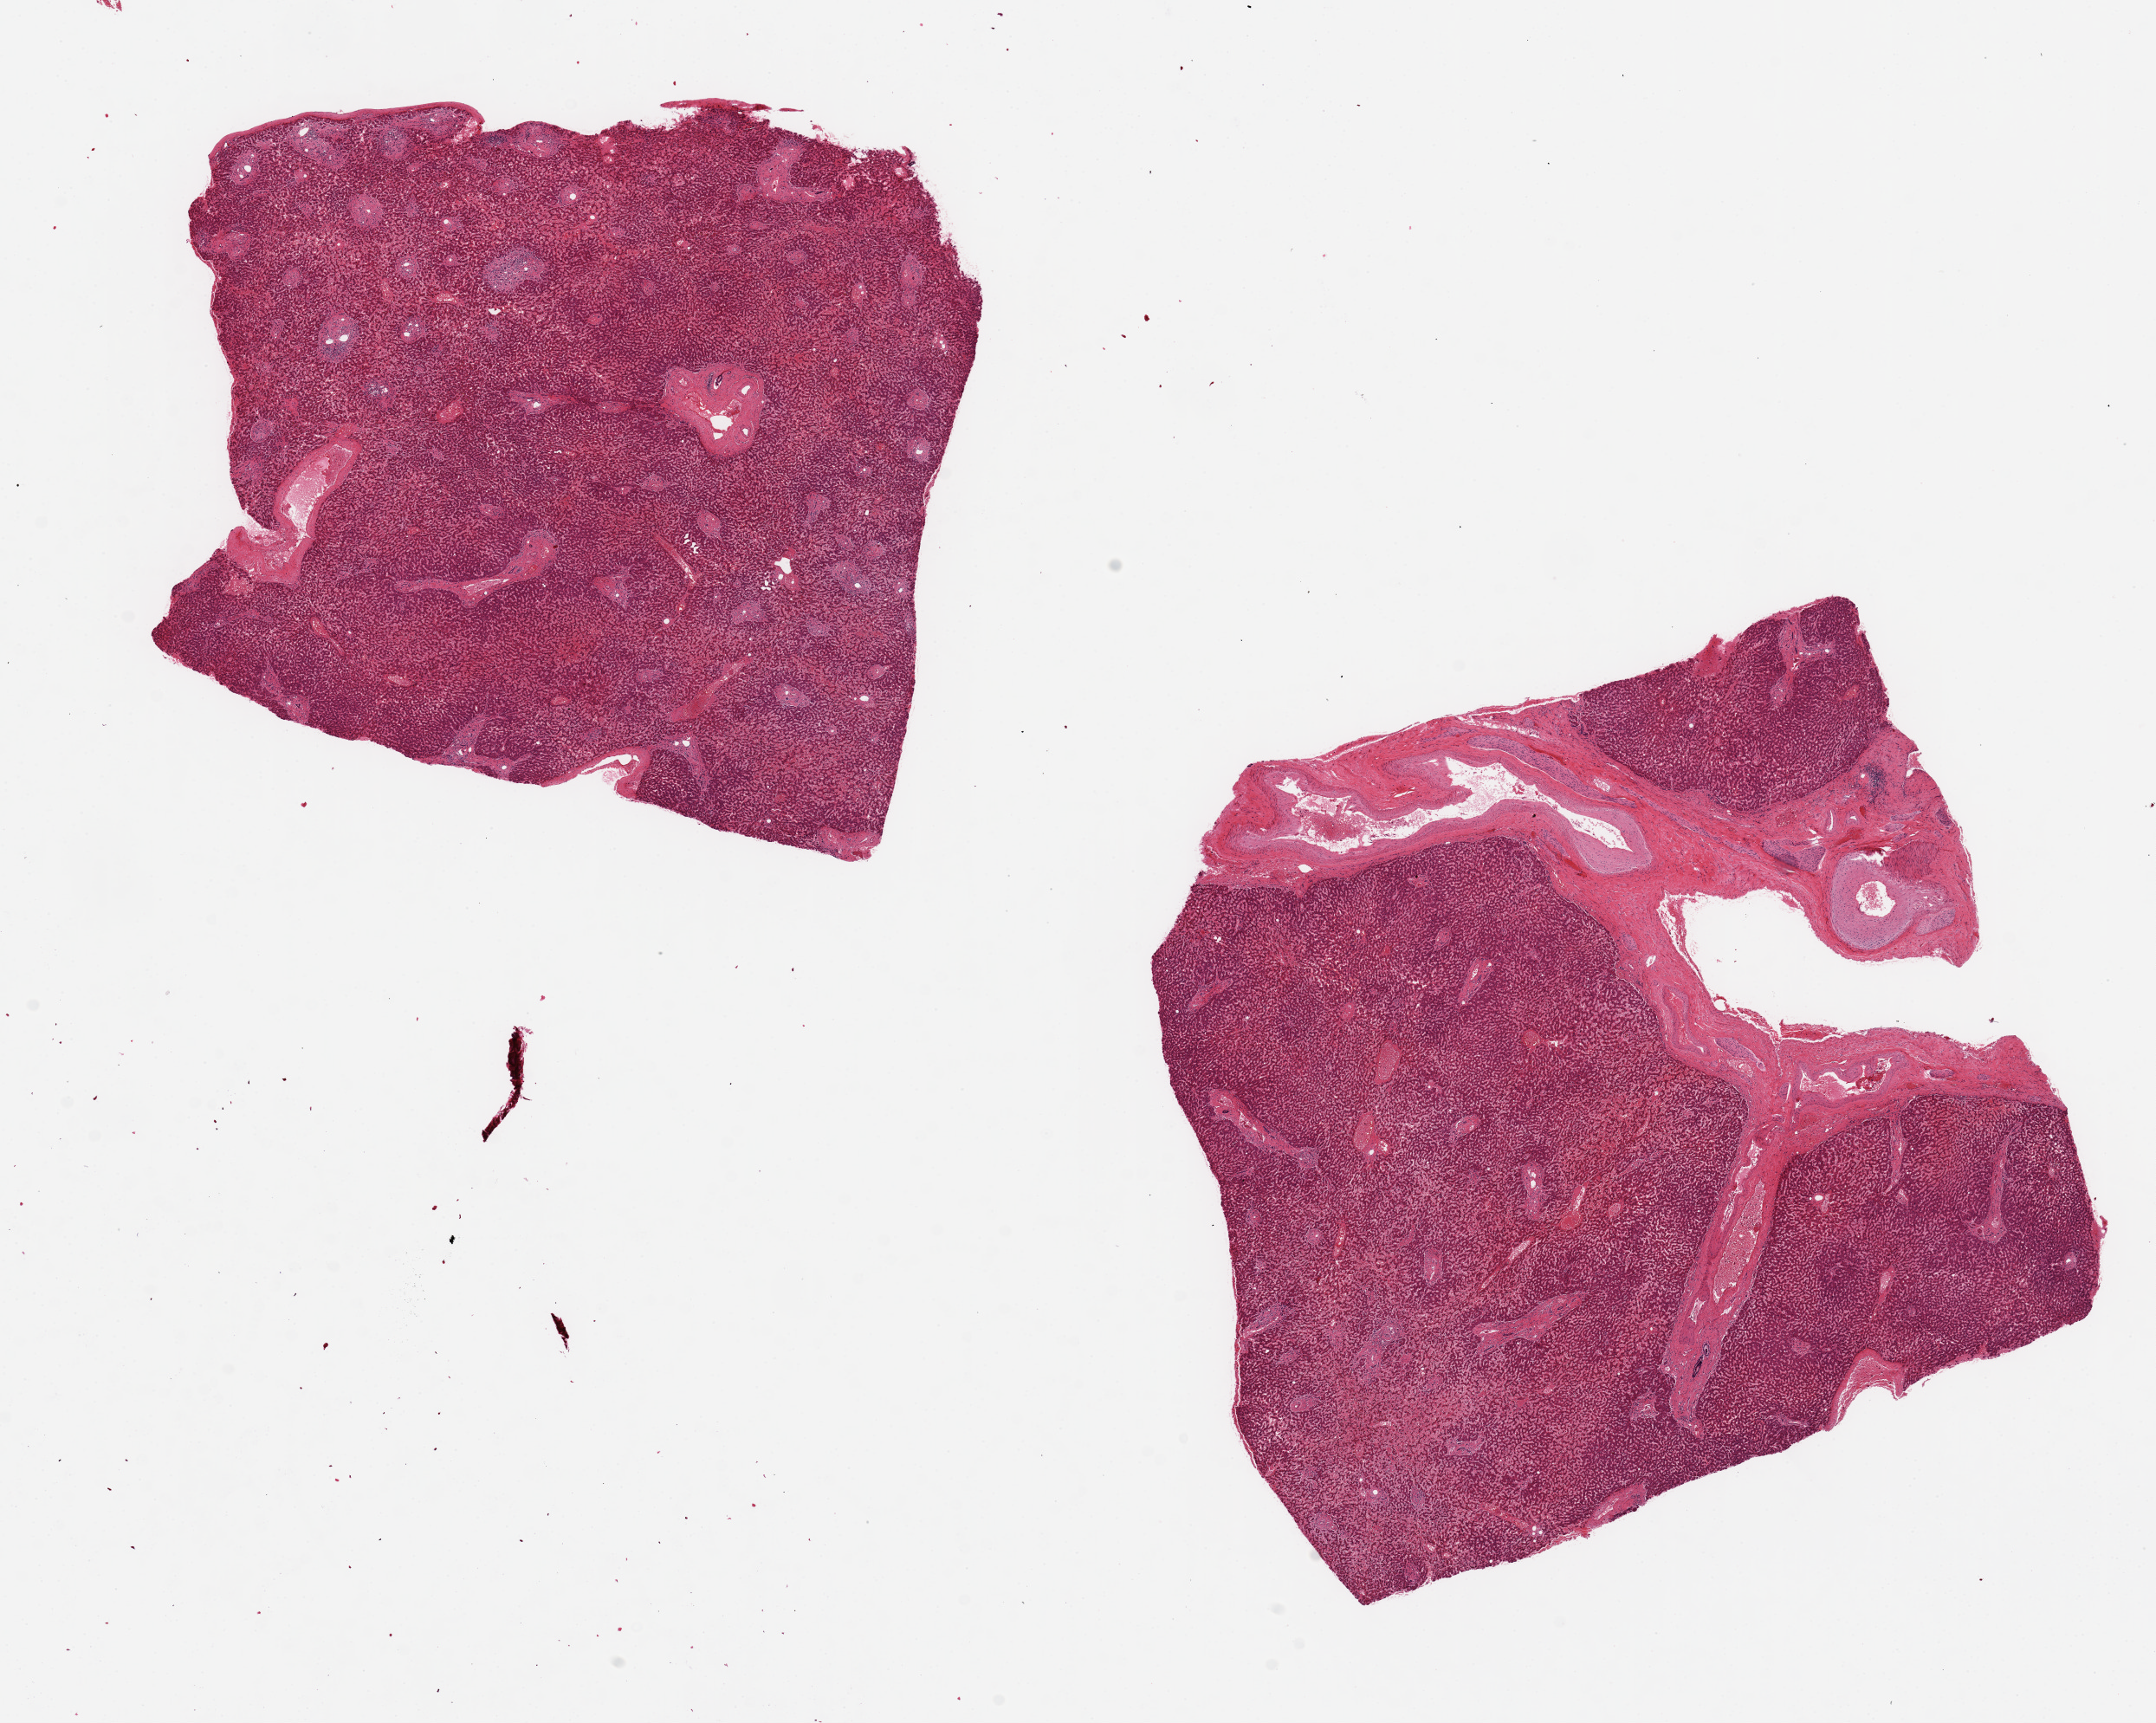
Digitized hematoxylin and eosin (H&E)-stained section — shown as a low-resolution overview of the whole scanned area (about 19.7 x 15.7 mm, from a 20x scan), PAXgene-fixed, paraffin-embedded tissue, section of liver (target tissue), donor tissue sample. Male donor.
• pathologist's review note for this sample: 2 pieces, 8x7.5 & 7x7mm; moderate congestion; some portal fibrosis